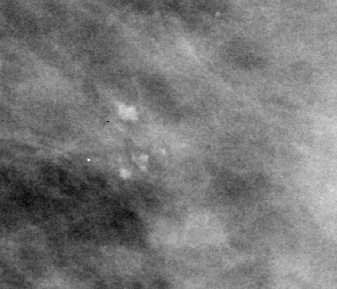
Crop from a digitized film mammogram around one marked abnormality; left breast; MLO view; BI-RADS breast density category 3 (scale 1–4).
Marked abnormality: calcifications, morphology pleomorphic, distribution clustered / segmental; BI-RADS assessment category 4; pathology (as recorded): benign.